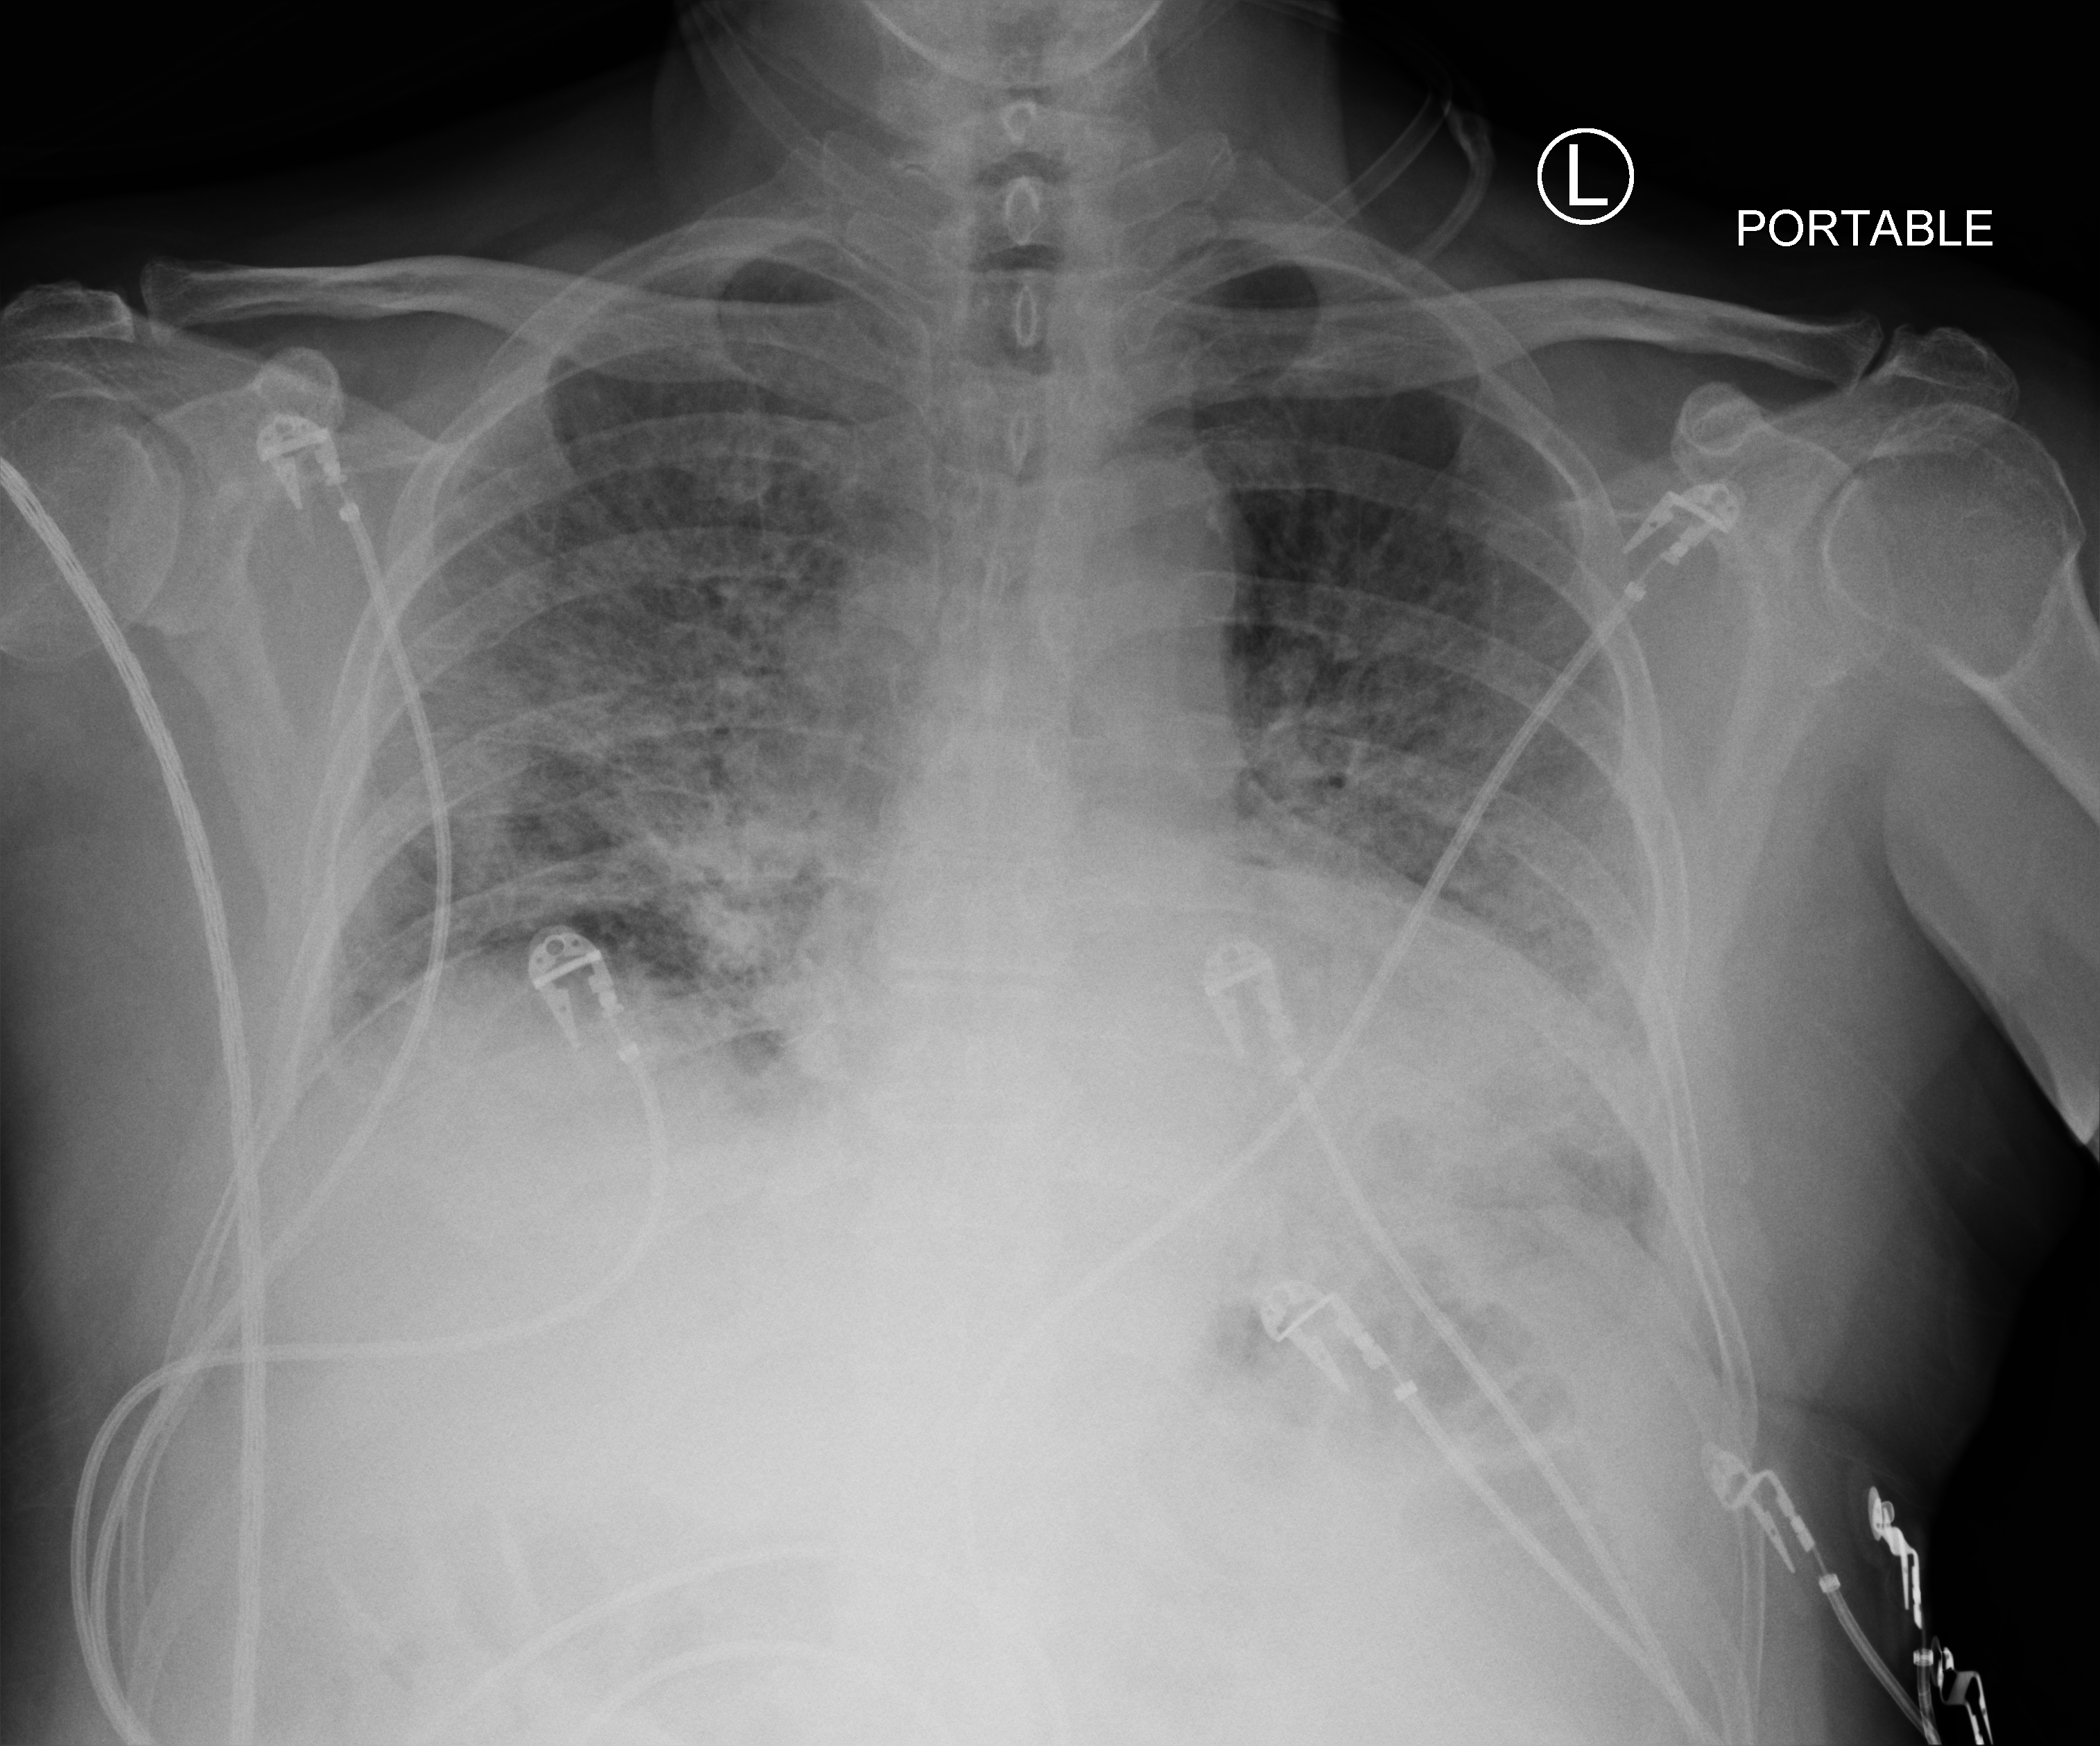
Chest X-ray (portable), anteroposterior (AP) projection. Male patient hospitalised with COVID-19, age 60–74 years.
From the hospital-stay record, not from the radiograph (when in the stay this image was taken is not recorded): length of hospital stay: 28 days; smoking status (admission record): never; mechanically ventilated during this hospital stay: yes.